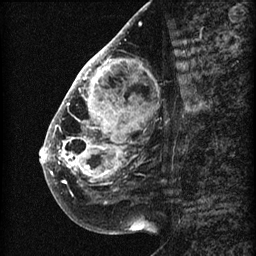
Breast MRI (dynamic contrast-enhanced), one sagittal slice; slice 26 of 60 in the series (ordered by position); 3 images stored at this slice position (order not interpretable as contrast timing); 1.5 T; TE 4.2 ms, TR 22.7 ms; 2 mm slice thickness; 256 × 256 image matrix, field of view 180 × 180 mm. Female patient, age 48 years. Case-level facts recorded for this patient, not image findings: setting: breast cancer imaged before/during neoadjuvant chemotherapy; receptor status: triple-negative.
Structures marked on this image (semi-automatic segmentation, software-assisted and operator-edited):
- analysis volume of interest (the breast-tissue region the enhancement analysis was run in; not a lesion): bounding box [x1, y1, x2, y2] px = [44, 30, 173, 207]
- tumour enhancement mask (voxels above the 90 % enhancement threshold inside the analysis volume of interest): [44, 31, 127, 185]